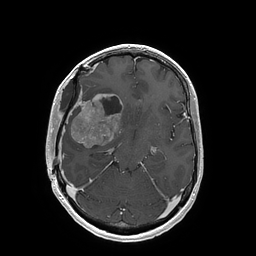
Brain MRI from a brain-tumour surgery series, one axial slice; position 101 of 202 along the scan axis; T1-weighted post-contrast; 1 mm slice thickness; 256 × 256 image matrix, field of view 250 × 250 mm. Case-level facts recorded for this patient, not image findings: histopathology: Glioblastoma; WHO grade: 4; IDH mutation: no.
Outlined on this slice (expert manual segmentation):
- tumour: box from (x=70, y=94) to (x=121, y=148) px